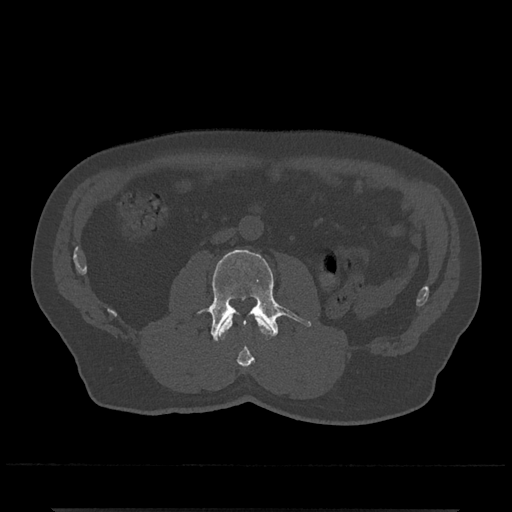
CT including the spine, one axial slice; position 239 of 797 along the scan axis; 120 kVp; bone window (W 1800 / L 400 HU); 0.5 mm slice thickness; 512 × 512 image matrix, field of view 393 × 393 mm. Patient: male, 67 years. Case-level facts recorded for this patient, not image findings: primary cancer: prostate.
Structures marked on this image (semi-automatically segmented with operator editing):
- L2 vertebra: bounding box [x1, y1, x2, y2] px = [218, 315, 271, 367]
- L3 vertebra: [207, 249, 311, 341]